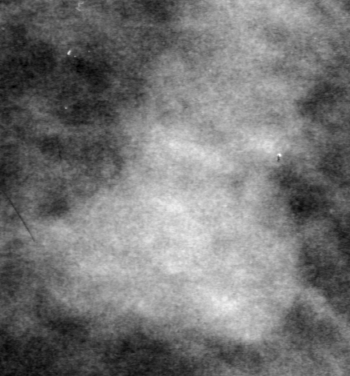
Region of interest cut from a scanned film mammogram (one marked finding); right breast; MLO view.
Mass, shape oval, margins ill defined; BI-RADS assessment category 4; subtlety rating 5 on a 1 (subtle) to 5 (obvious) scale; pathology (as recorded): malignant.